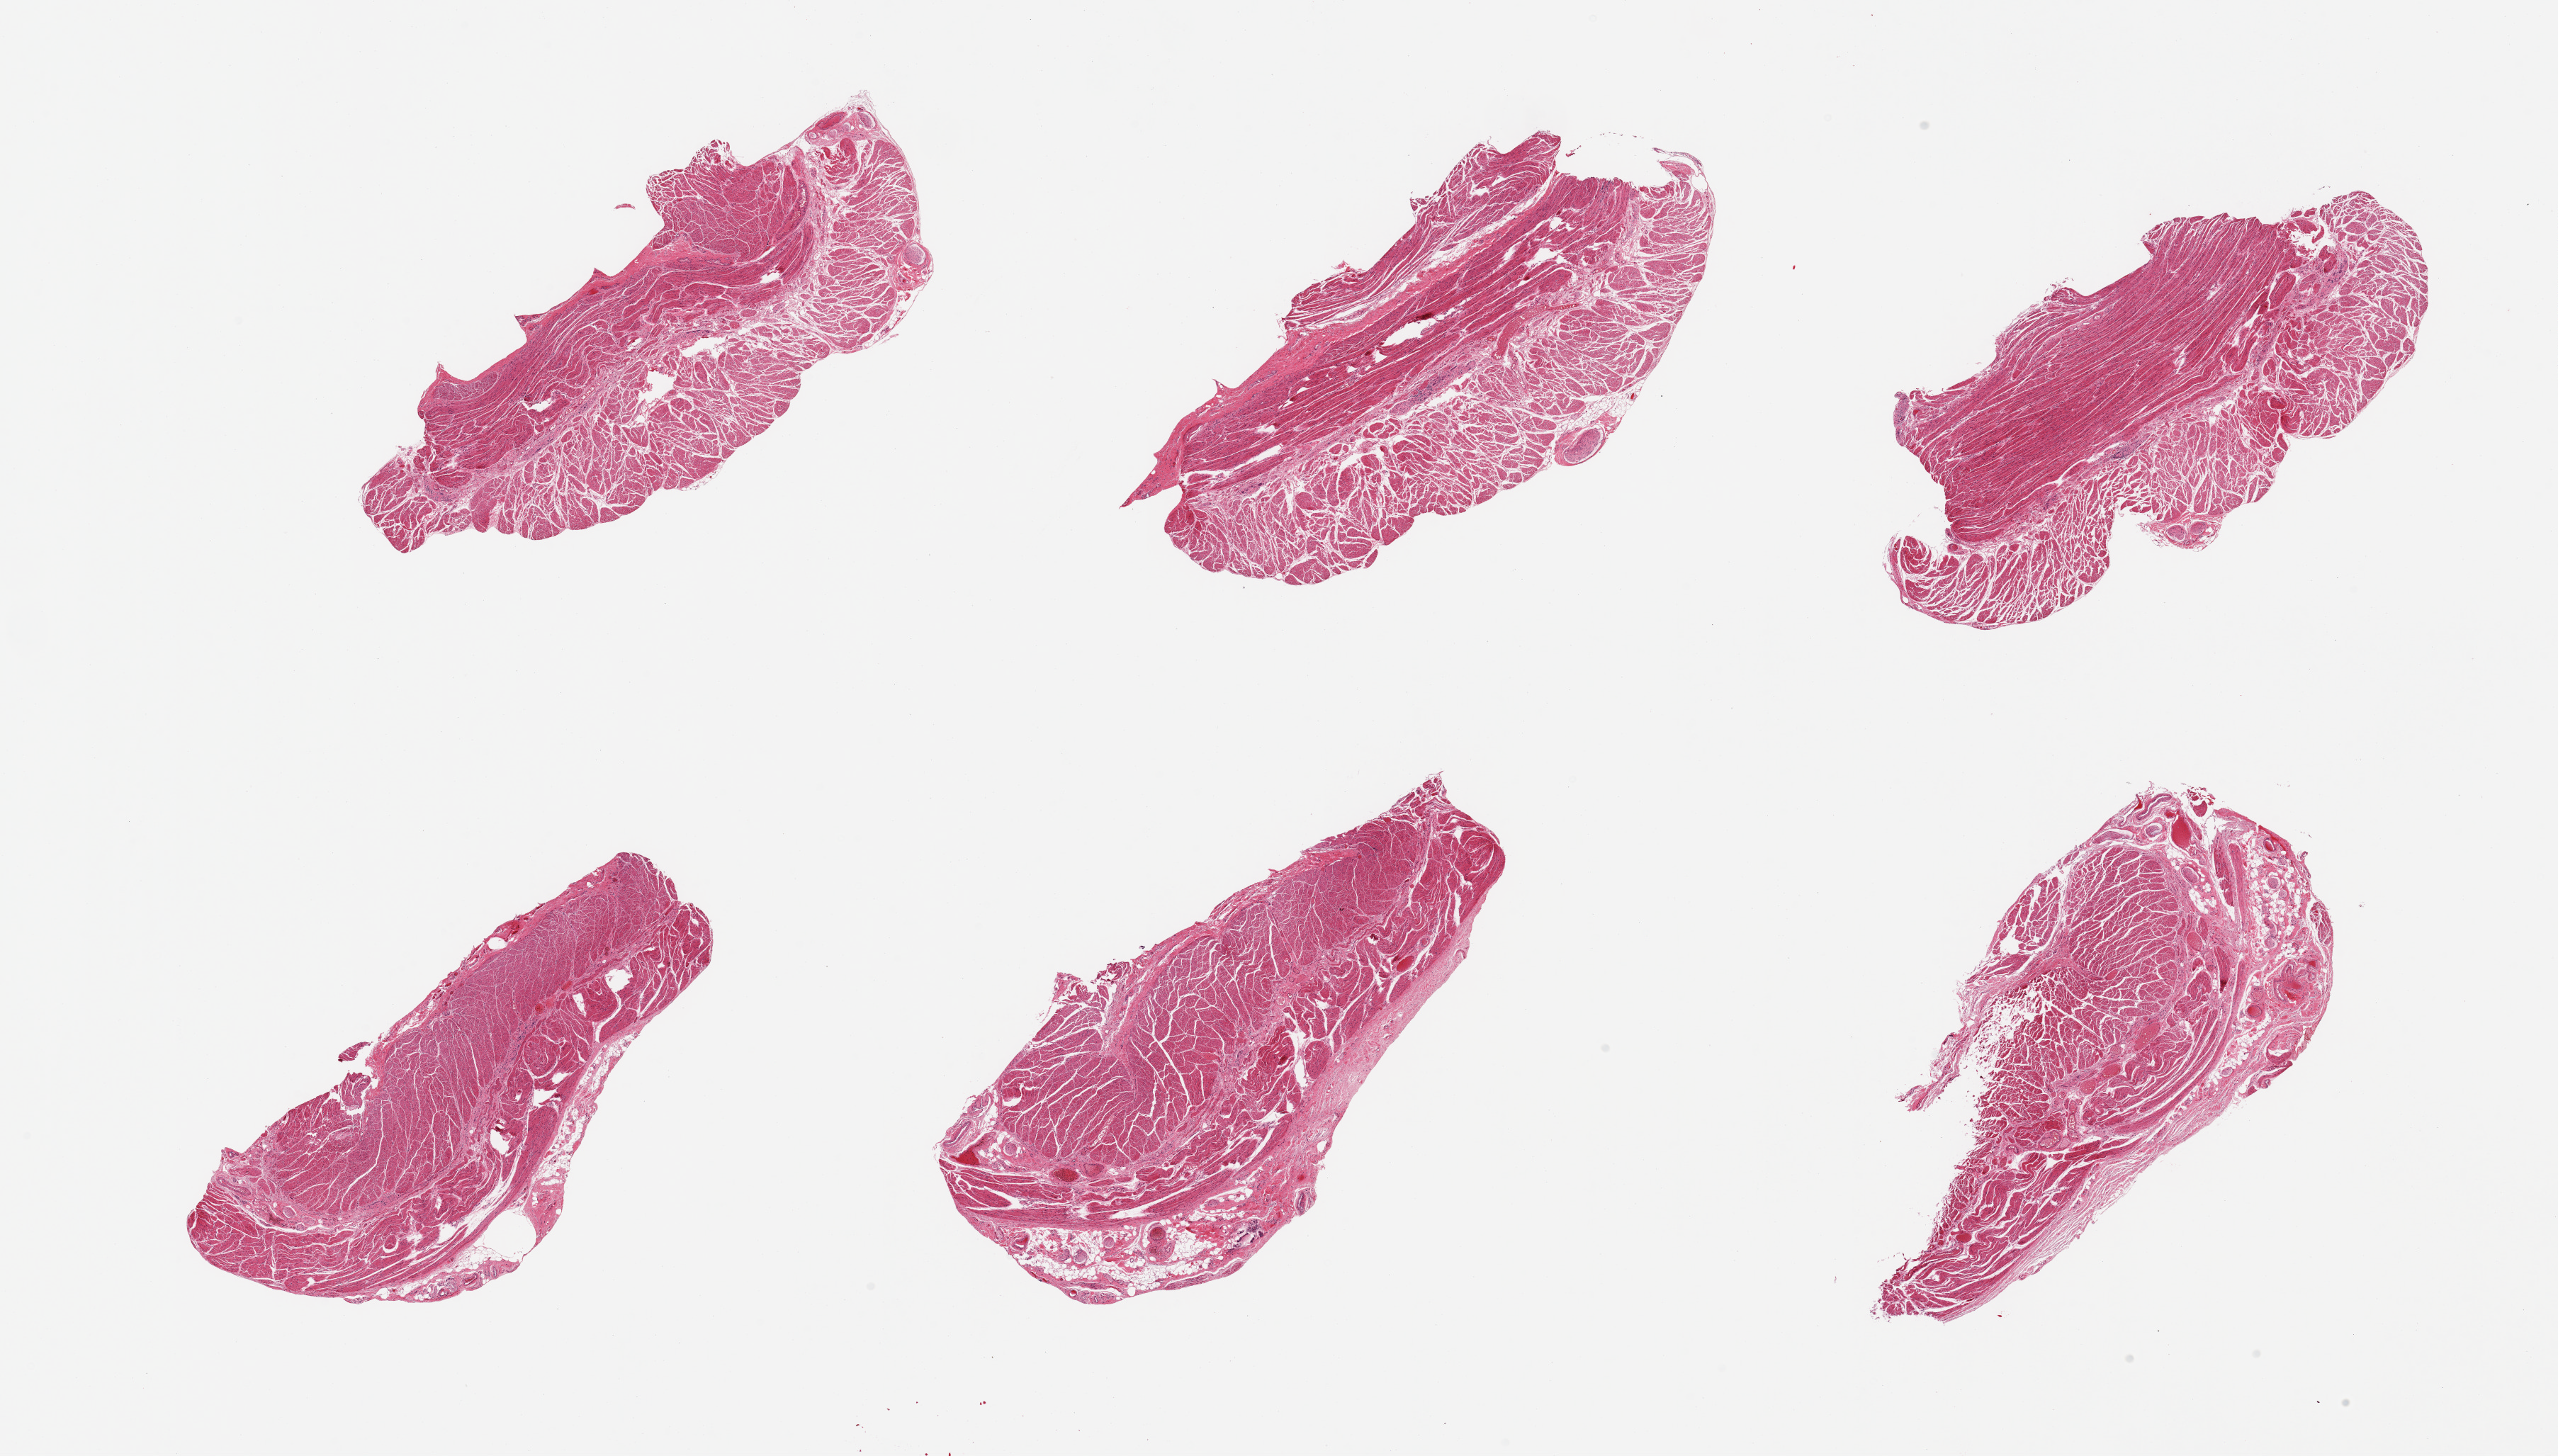
Haematoxylin and eosin whole-slide image, brightfield, low-resolution overview of the scanned area, about 28.5 x 16.3 mm; PAXgene-fixed, paraffin-embedded tissue; section of esophageal muscle (target tissue); donor tissue sample. Donor: female.
Review note (as recorded): 6 pieces; well dissected.